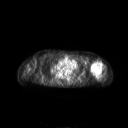
FDG PET of an extremity soft-tissue mass (from a PET/CT study), one axial slice. Slice 174 of 267 in the series (ordered by position). 3.27 mm slice thickness. 128 × 128 image matrix, field of view 700 × 700 mm. Patient: female, 83 years. Case-level facts recorded for this patient, not image findings: histological type: pleiomorphic leiomyosarcoma; grade: high; site of the primary tumour: left biceps.
Outlined on this slice (expert contour drawn on MRI and transferred to this co-registered scan by the dataset authors):
- gross tumour volume including surrounding oedema: bounding box <90,59,103,77> (left, top, right, bottom; pixels)
- gross tumour volume (mass): <90,60,102,75>